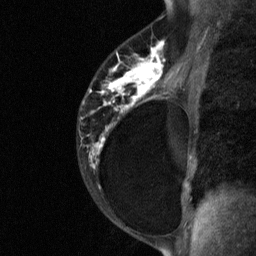
Breast MRI (dynamic contrast-enhanced), one sagittal slice; position 43 of 64 along the scan axis; dynamic contrast-enhanced study with each time point stored as its own series, time point 2 of 3 at this slice position (early post-contrast, ordered by acquisition time); 1.5 T; TE 4.8 ms, TR 27 ms; 2 mm slice thickness; 256 × 256 image matrix. Patient: female, 34 years. Case-level facts recorded for this patient, not image findings: setting: breast cancer imaged before/during neoadjuvant chemotherapy; receptor status: HR-positive, HER2-negative.
Outlined on this slice (semi-automatically segmented with operator editing):
- analysis volume of interest (the breast-tissue region the enhancement analysis was run in; not a lesion): box from (x=78, y=44) to (x=181, y=191) px
- tumour enhancement mask (voxels above the 90 % enhancement threshold inside the analysis volume of interest): (x=90, y=44)–(x=166, y=168)